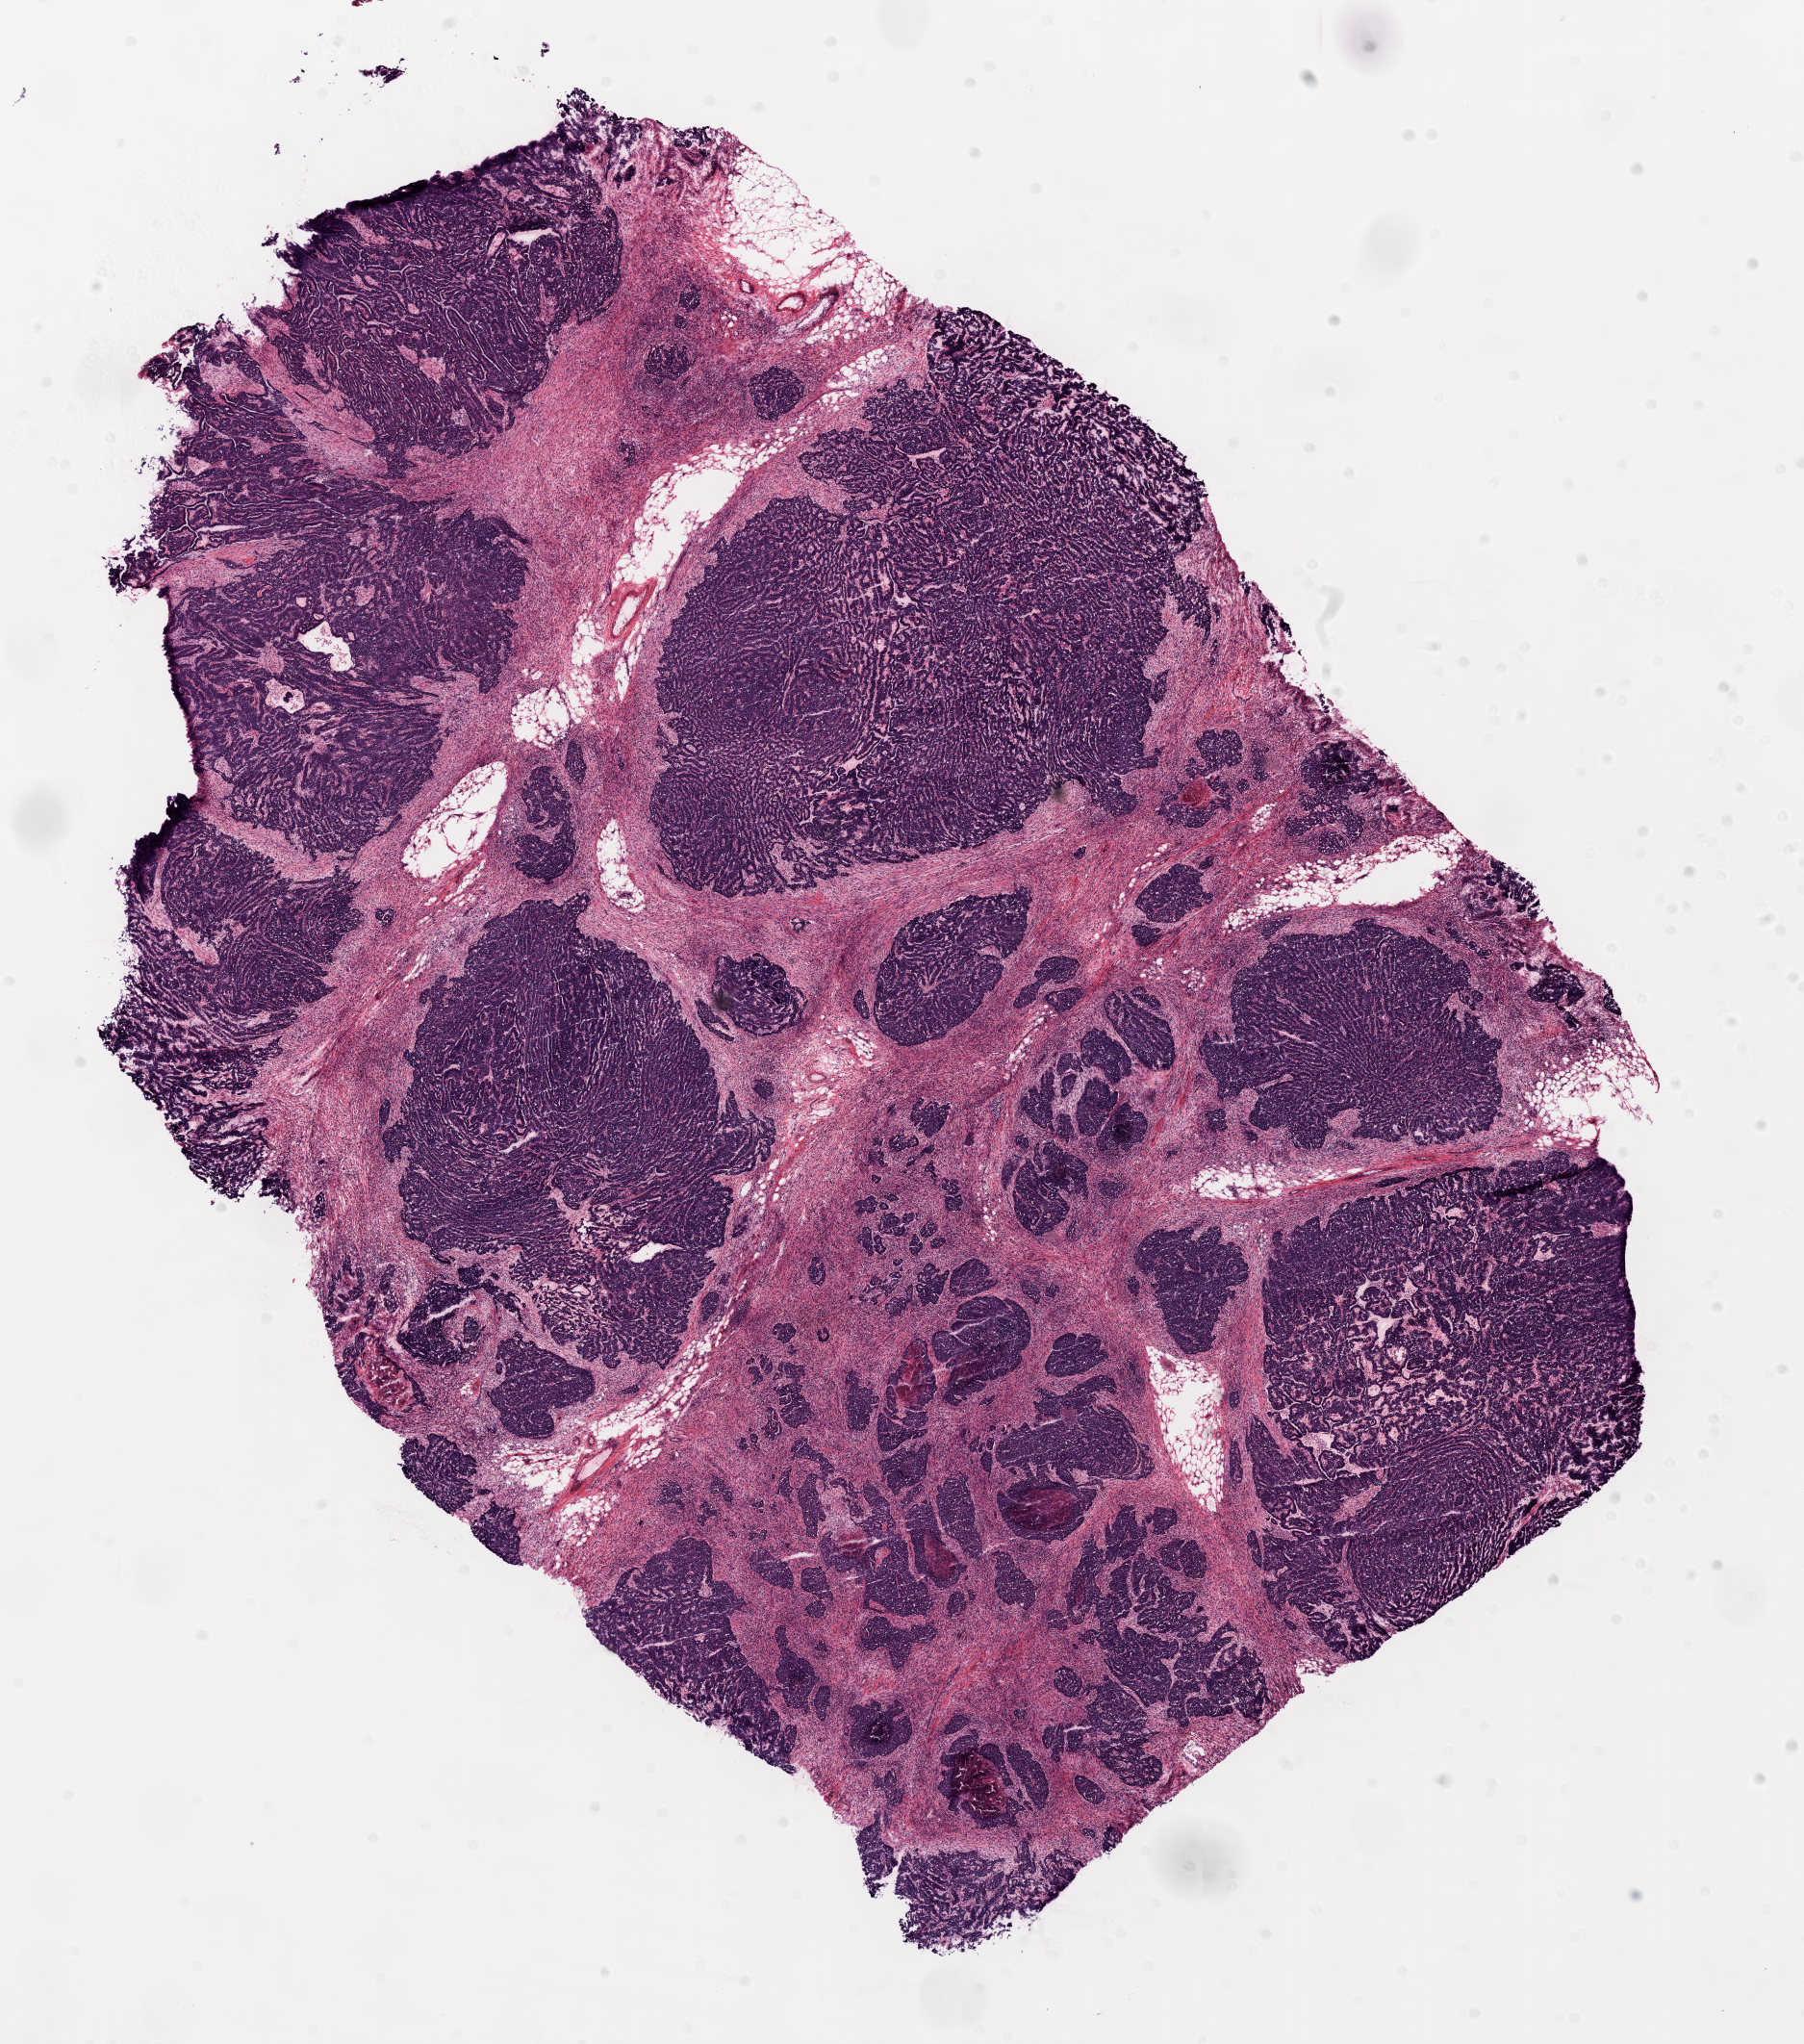
Whole-slide histology image, H&E-stained — shown as a low-resolution overview of the whole scanned area (about 15.0 x 17.0 mm), frozen section from the top of the tissue portion, sample: primary tumour, ovary. Female patient; age at initial diagnosis 48 years. Histologic grade: G3 (poorly differentiated). Slide review estimates, as recorded: tumour cells 75%, tumour nuclei 80%, normal cells 0%, stromal cells 20%, necrosis 5%.
Pathologic diagnosis: Serous cystadenocarcinoma, NOS. Laterality: bilateral. FIGO stage: IIIC.